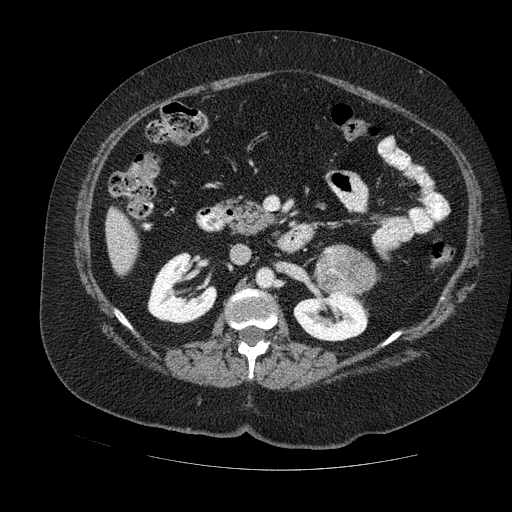
Contrast-enhanced abdominal CT, one axial slice. Position 57 of 121 along the scan axis. Soft-tissue window (W 400 / L 40 HU). 2.5 mm slice thickness. 512 × 512 image matrix, field of view 420 × 420 mm. Female patient. Case-level facts recorded for this patient, not image findings: diagnosis: adrenocortical carcinoma; tumour side: left adrenal.
Structures marked on this image (semi-automatic segmentation, software-assisted and operator-edited):
- mass: box from (x=320, y=245) to (x=375, y=294) px